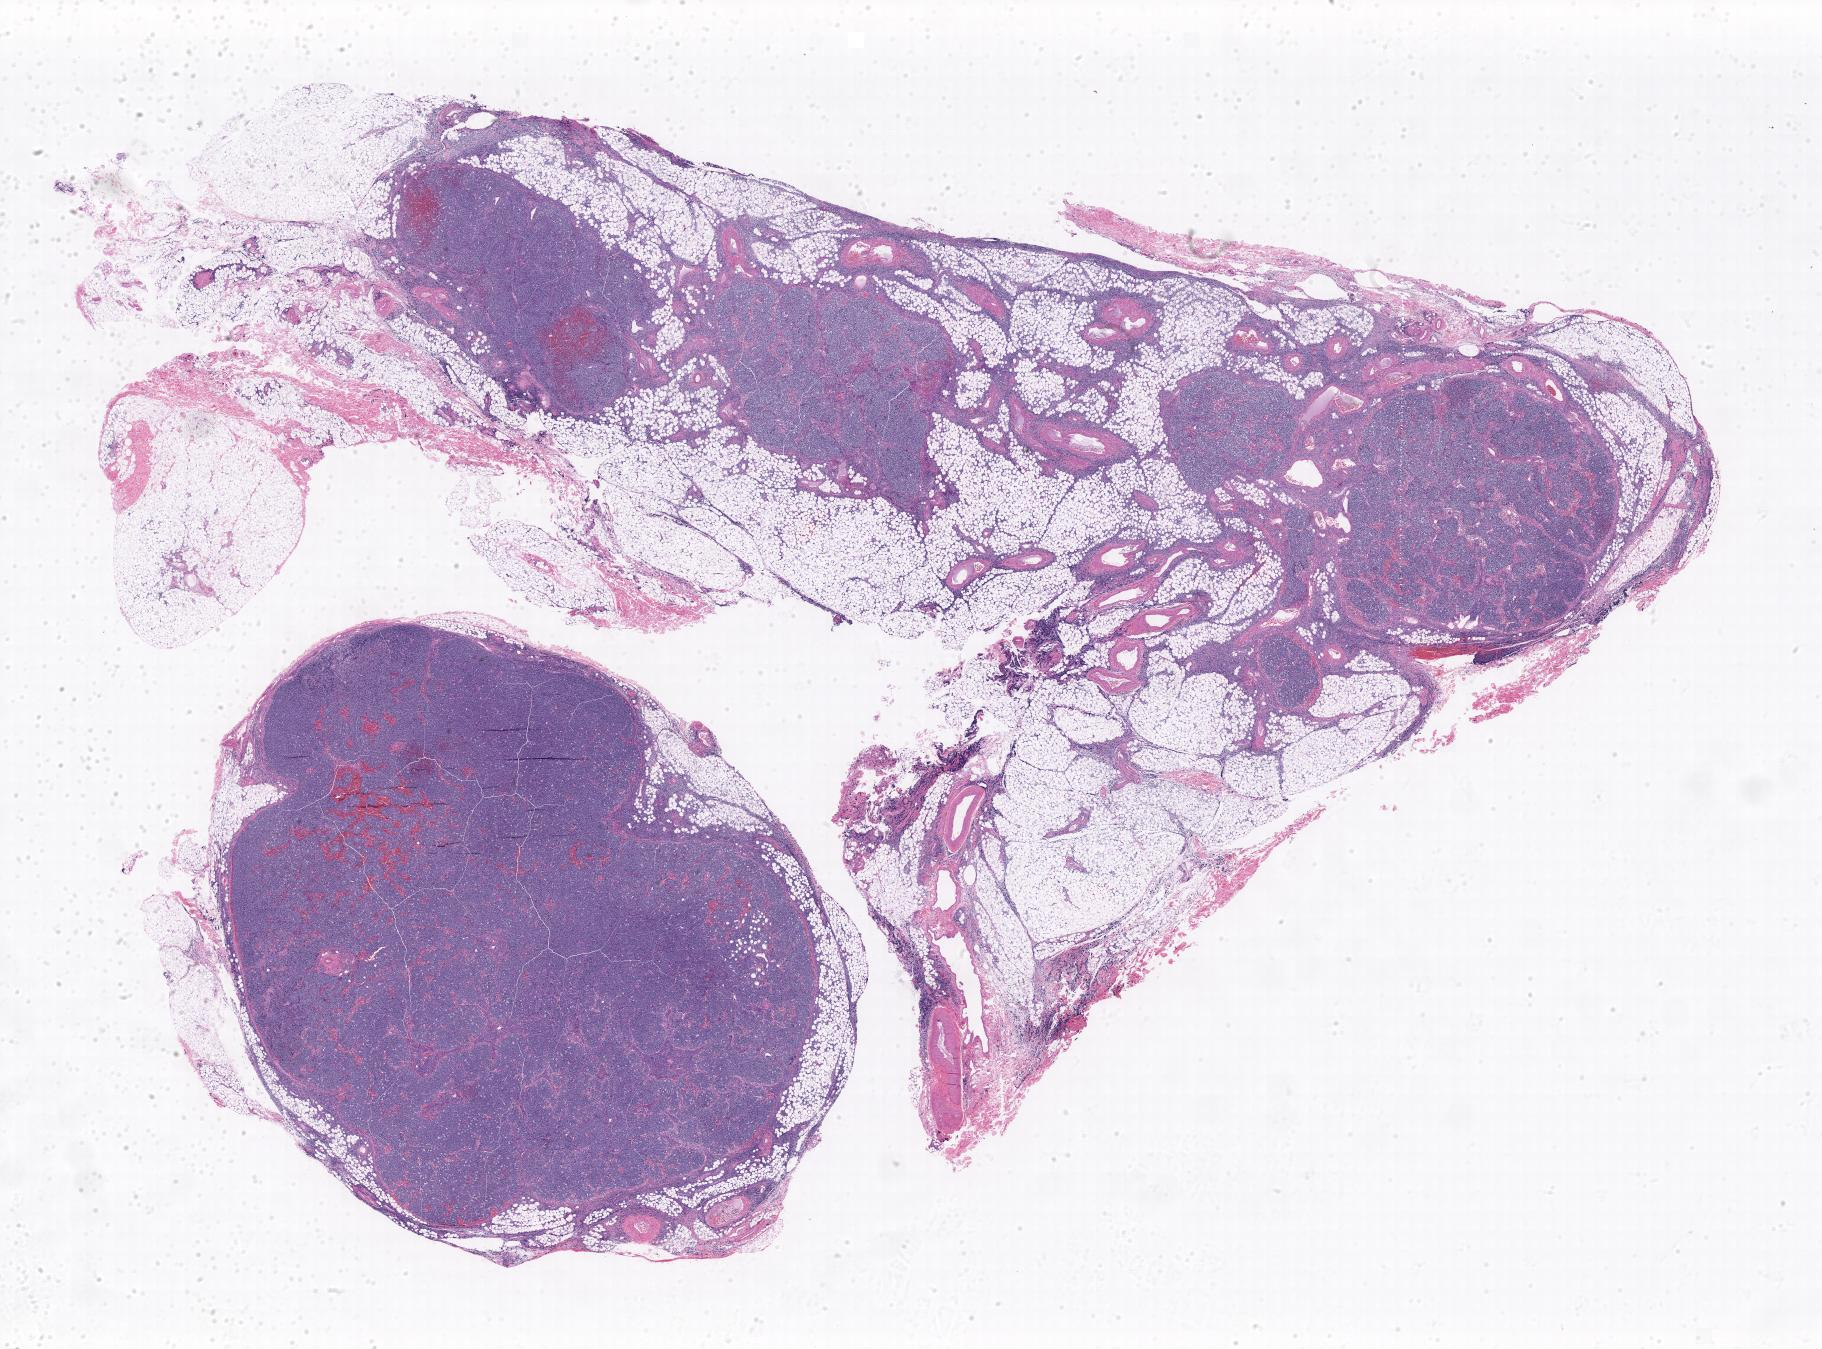
Whole-slide image, hematoxylin and eosin (H&E) stain — whole scanned area shown as a low-resolution overview, specimen: tumor tissue, anatomic site: spleen. Patient female; age 15 years.
Diagnosis: Burkitt lymphoma, NOS.